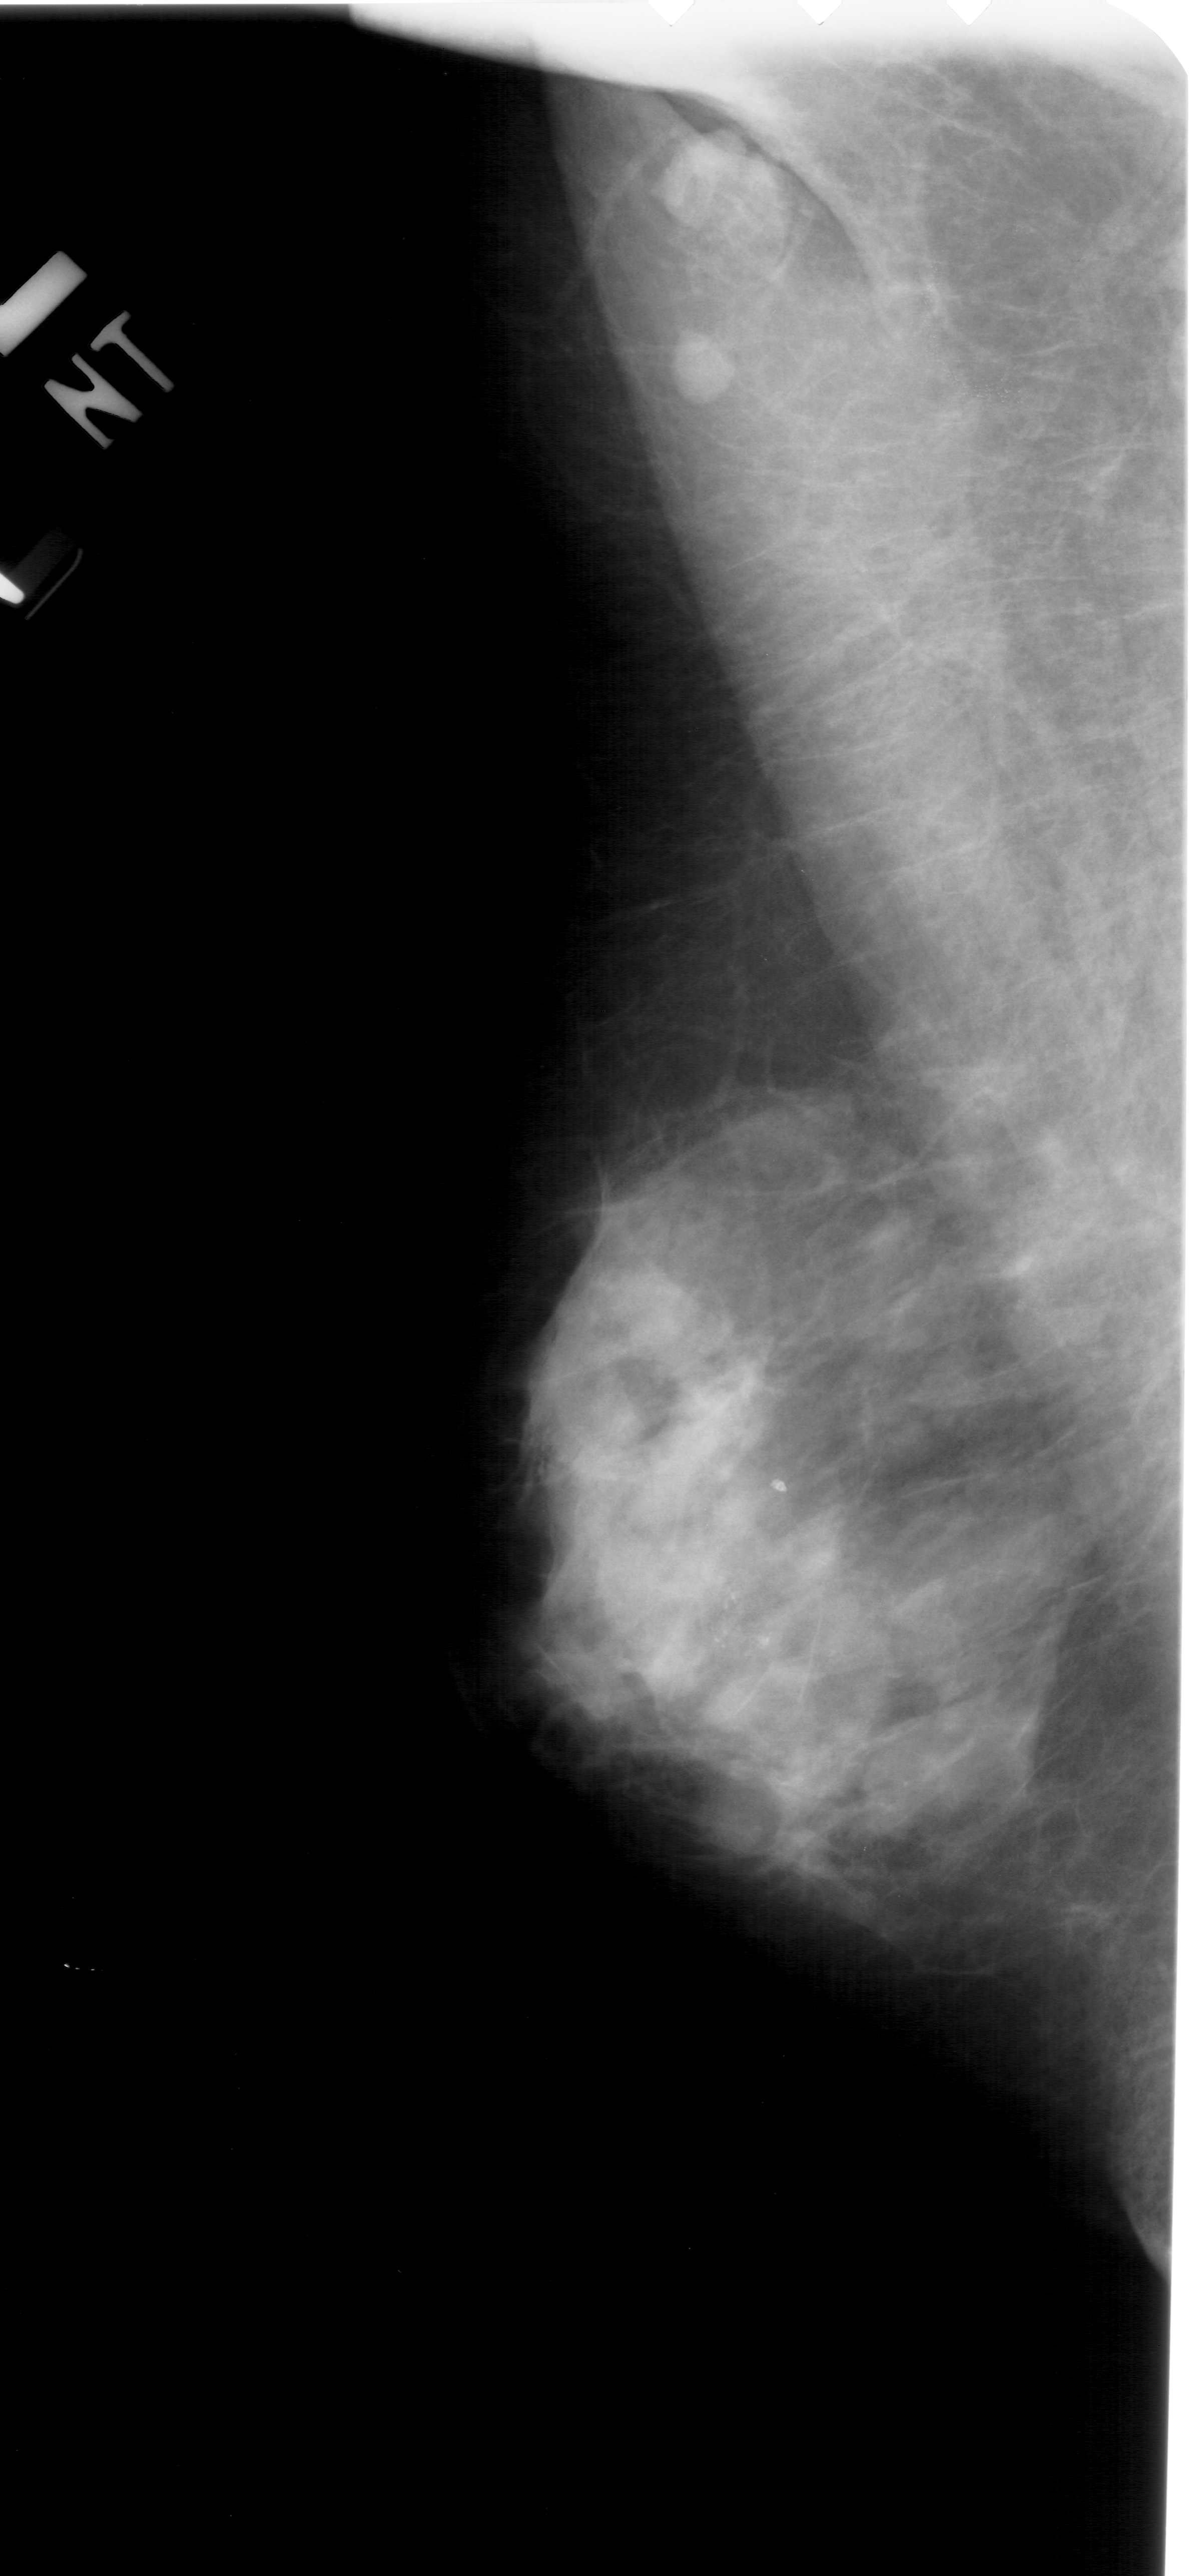
Scanned film-screen mammogram; left breast; mediolateral oblique (MLO) view; breast composition: extremely dense (BI-RADS density category 4 of 4); 1194 × 2576 image matrix.
Expert-marked regions of interest on this image (one box per marked abnormality):
- calcifications, morphology pleomorphic, distribution clustered; BI-RADS assessment category 4; pathology (as recorded): malignant: bounding box <702,1573,785,1666> (left, top, right, bottom; pixels)